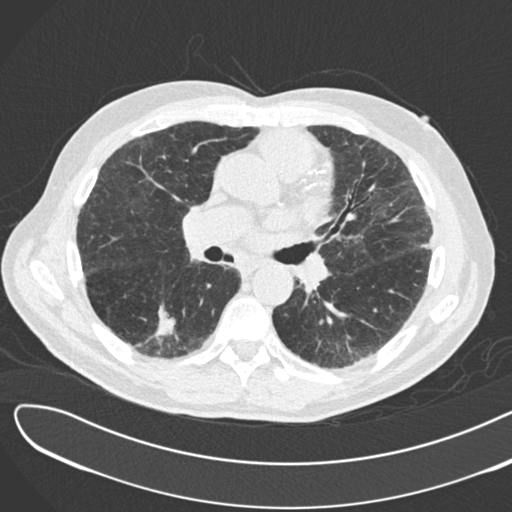
Low-dose screening chest CT, one axial slice. Slice 93 of 183 in the series (ordered by position). Reconstruction kernel B30f. 120 kVp. Lung window (W 1500 / L -600 HU). 512 × 512 image matrix, field of view 370 × 370 mm.
Structures marked on this image (outlined manually by an expert reader):
- lesion 1 (tumor, lower lobe of right lung): bounding box (x1, y1, x2, y2) in pixels: (155, 304, 176, 341)